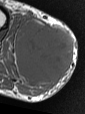
MRI of an extremity soft-tissue mass, one axial slice; position 26 of 47 along the scan axis; MR volume resampled by the dataset authors to the PET/CT grid (not the native acquisition matrix); 3.27 mm slice thickness; 85 × 114 image matrix. Male patient. Case-level facts recorded for this patient, not image findings: histological type: pleiomorphic liposarcoma; grade: high; site of the primary tumour: right calf.
Structures marked on this image (expert contour drawn on MRI and transferred to this co-registered scan by the dataset authors):
- gross tumour volume including surrounding oedema: bounding box [x1, y1, x2, y2] px = [15, 23, 73, 86]
- gross tumour volume (mass): [15, 23, 73, 83]